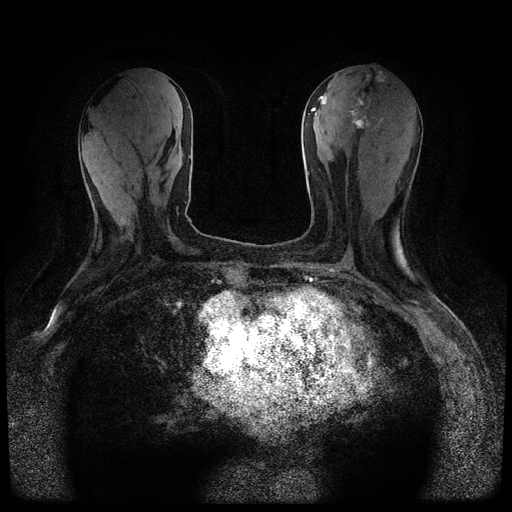
Breast MRI (dynamic contrast-enhanced, multi-phase), one axial slice; slice 29 of 116 in the series (ordered by position); dynamic contrast-enhanced series, time point 2 of 5 at this slice position (early post-contrast); 1.5 T; TE 2.7 ms, TR 5.4 ms; 2 mm slice thickness; 512 × 512 image matrix. Female patient, age 80 years.
Structures marked on this image (semi-automatic segmentation, software-assisted and operator-edited):
- breast lesion (labelled 'tumour' in the annotation; benign lesions carry a separate 'benign' label): box from (x=351, y=71) to (x=386, y=129) px